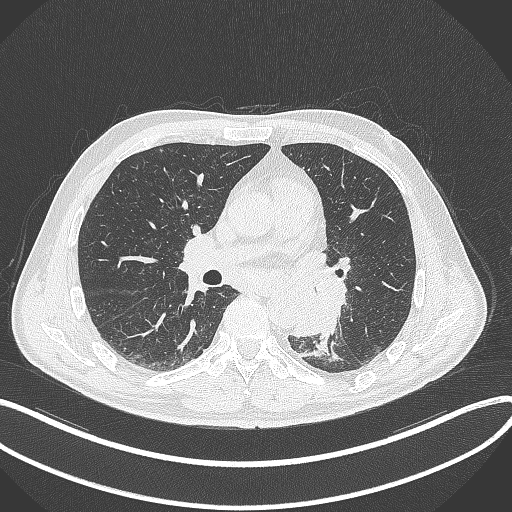
Chest CT, one axial slice; position 179 of 329 along the scan axis; reconstruction kernel B70f; 120 kVp; lung window (W 1500 / L -600 HU); 1 mm slice thickness; 512 × 512 image matrix. Patient: male, 59 years. Case-level facts recorded for this patient, not image findings: clinical TNM (as recorded): T2a N2 M0.
Annotated regions visible in this slice (bounding box drawn by a radiologist):
- lung tumour (recorded histology: squamous cell carcinoma): box from (x=286, y=269) to (x=346, y=339) px